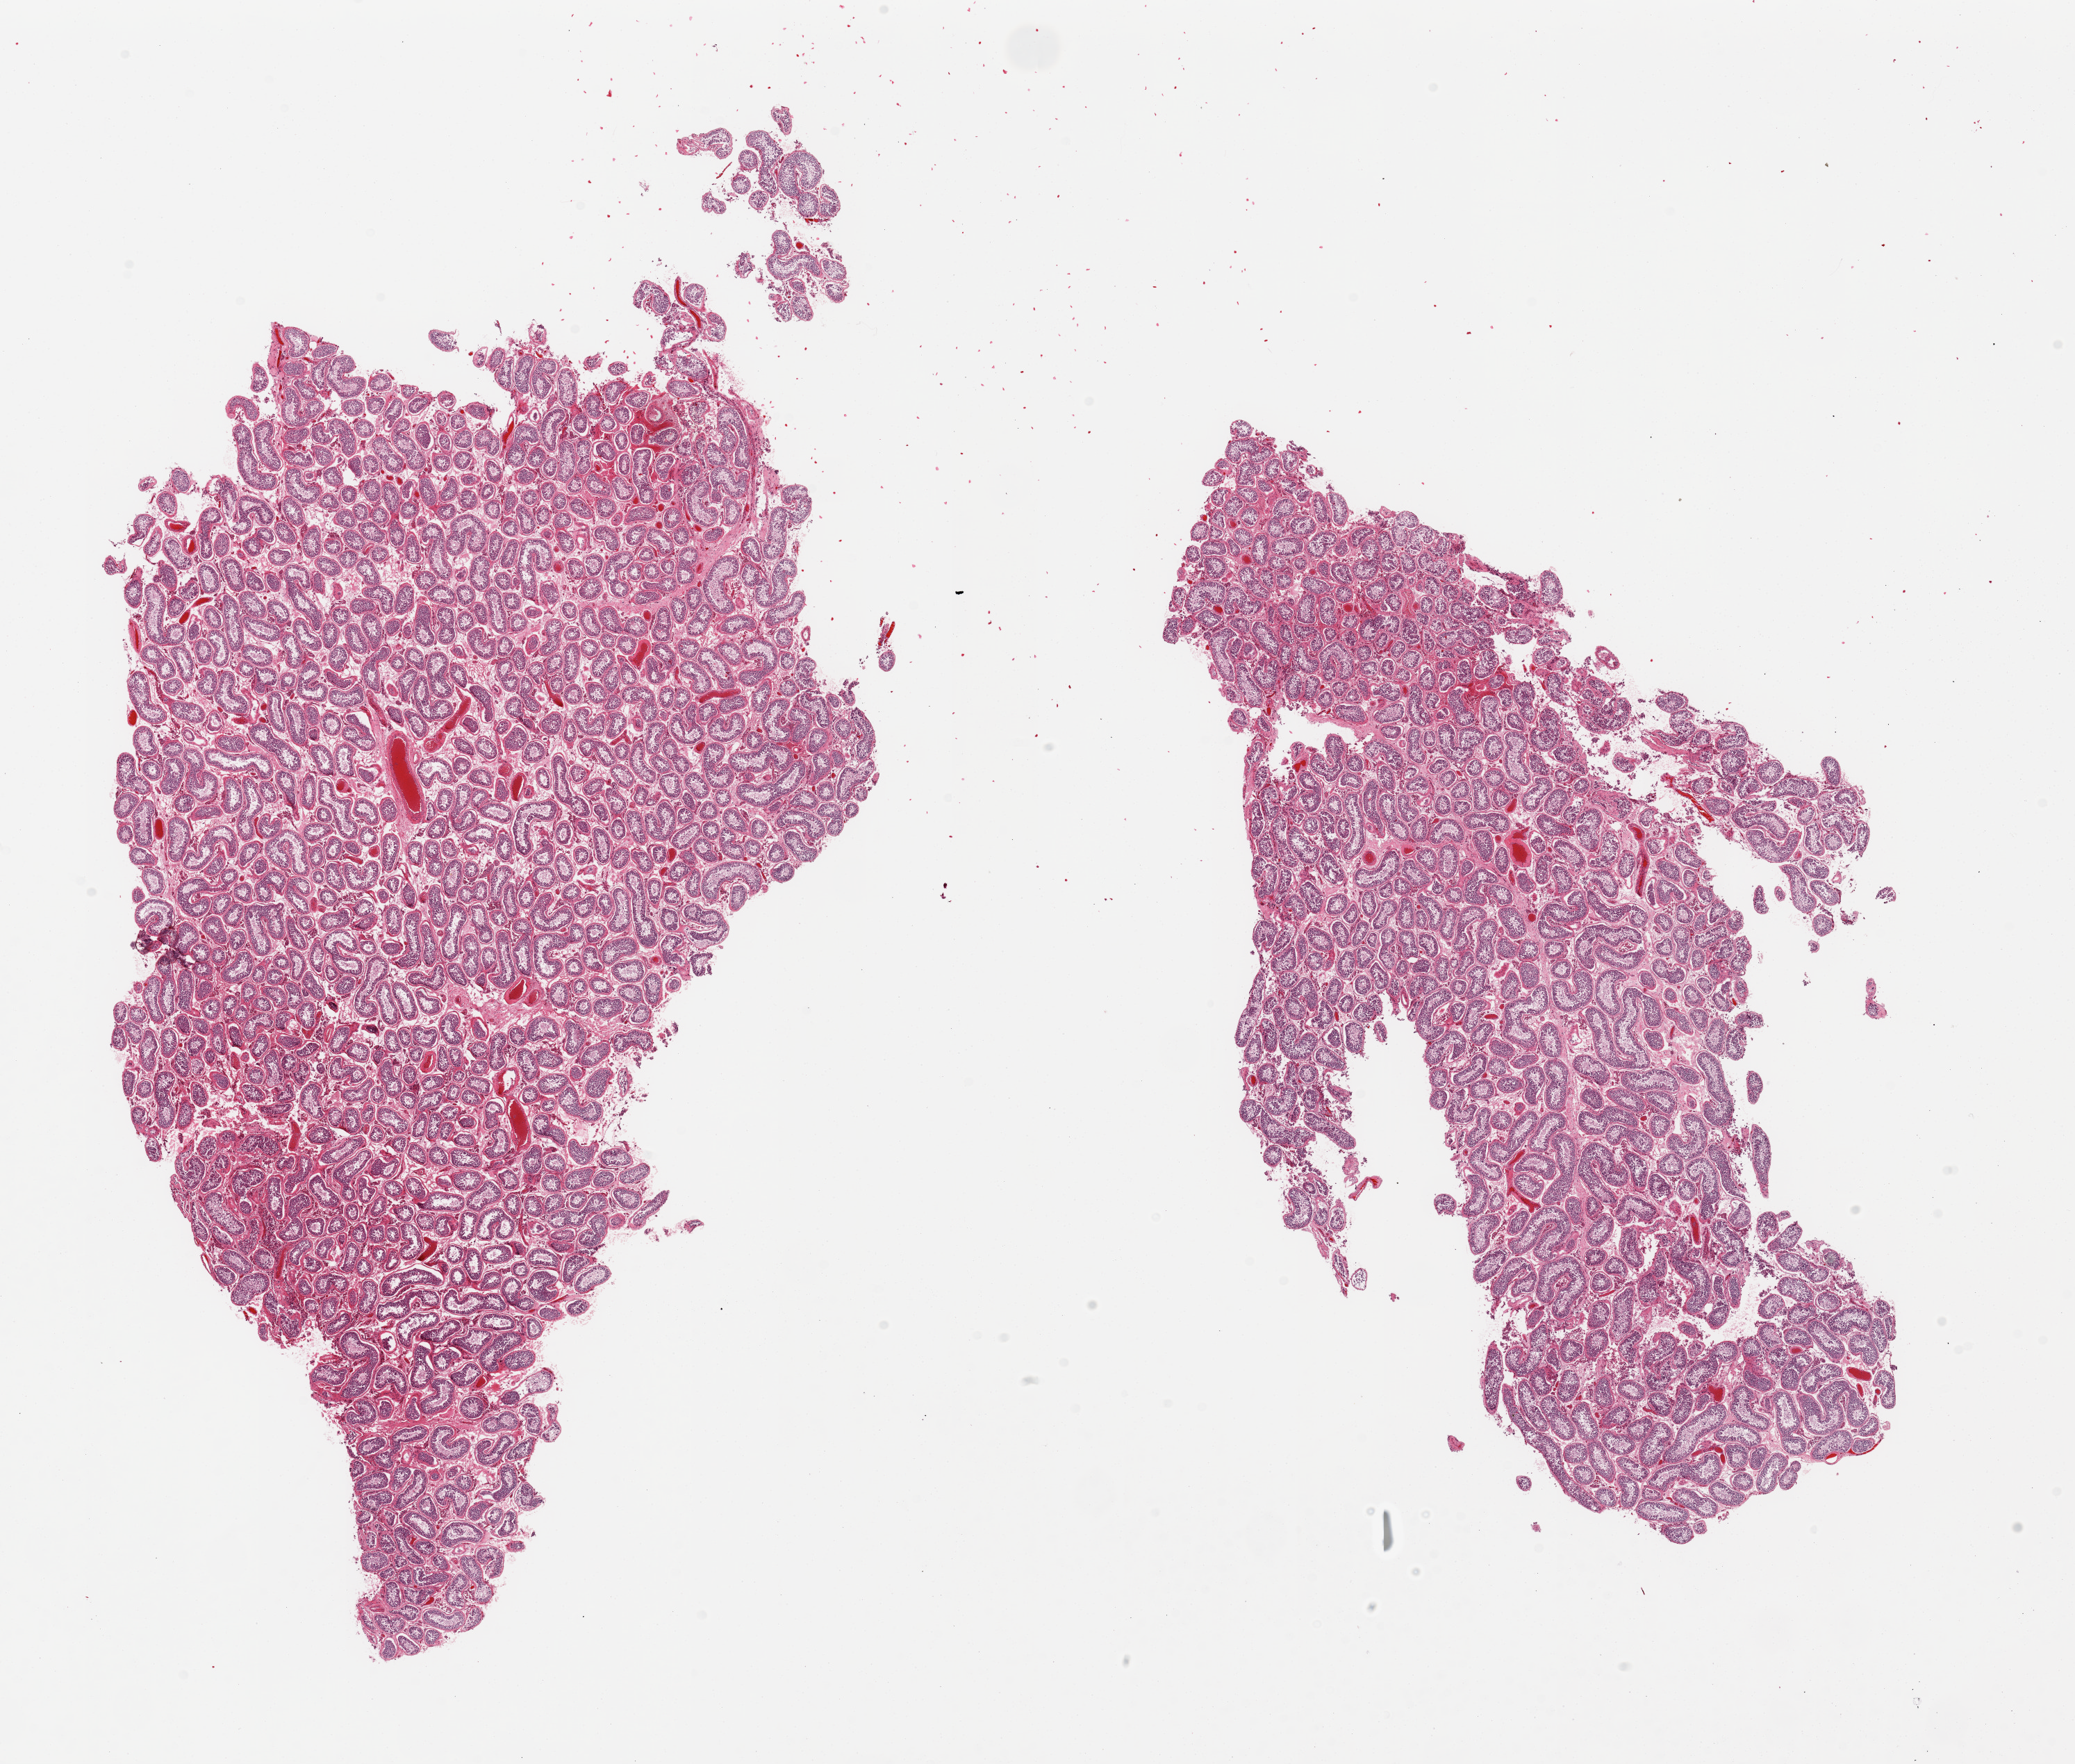
Digitized hematoxylin and eosin (H&E)-stained section, low-resolution overview of the scanned area, about 23.6 x 20.1 mm (from a 20x scan). PAXgene-fixed, paraffin-embedded tissue. Sampled site (target tissue): testis. Donor tissue sample. Donor: male.
Pathologist's review note for this sample: 2 pieces; spermatogenesis.